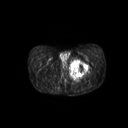
FDG PET of an extremity soft-tissue mass (from a PET/CT study), one axial slice. Slice 36 of 267 in the series (ordered by position). 128 × 128 image matrix, field of view 600 × 600 mm. Male patient, age 59 years. Case-level facts recorded for this patient, not image findings: histological type: pleiomorphic liposarcoma; grade: high; site of the primary tumour: left thigh.
Annotated regions visible in this slice (expert contour drawn on MRI and transferred to this co-registered scan by the dataset authors):
- gross tumour volume including surrounding oedema: bounding box <69,59,88,79> (left, top, right, bottom; pixels)
- gross tumour volume (mass): <69,60,87,77>